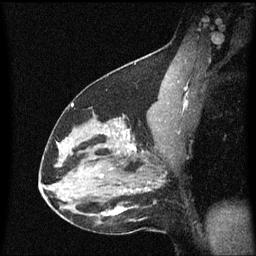
Breast MRI (dynamic contrast-enhanced), one sagittal slice. Slice 36 of 60 in the series (ordered by position). Dynamic contrast-enhanced series, image 2 of 3 at this slice position (ordered by acquisition). 1.5 T. TE 4.2 ms, TR 8.4 ms. 2 mm slice thickness. 256 × 256 image matrix, field of view 200 × 200 mm. Female patient, age 38 years. Case-level facts recorded for this patient, not image findings: setting: breast cancer imaged before/during neoadjuvant chemotherapy; receptor status: HR-positive, HER2-negative.
Annotated regions visible in this slice (semi-automatic segmentation, software-assisted and operator-edited):
- analysis volume of interest (the breast-tissue region the enhancement analysis was run in; not a lesion): bounding box [x1, y1, x2, y2] px = [122, 126, 154, 163]
- tumour enhancement mask (voxels above the 70 % enhancement threshold inside the analysis volume of interest): [128, 130, 137, 151]